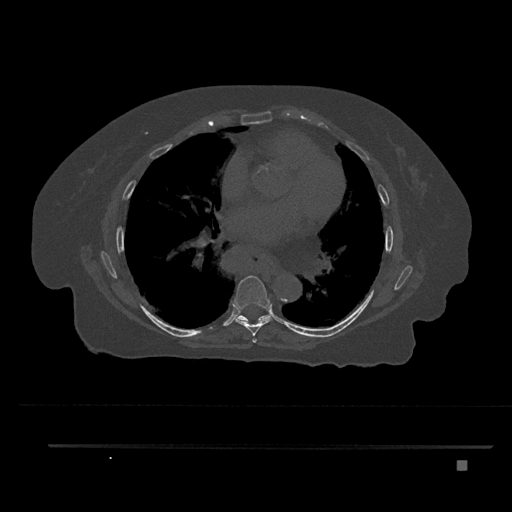
CT including the spine, one axial slice. Reconstruction kernel Br40s/3. 120 kVp. Bone window (W 1800 / L 400 HU). 0.5 mm slice thickness. 512 × 512 image matrix, field of view 437 × 437 mm. Female patient, age 76 years. From the clinical record (not read from this slice): primary cancer: lung; vertebrae with lytic lesions (as recorded): T11, L3.
Outlined on this slice (semi-automatic segmentation, software-assisted and operator-edited):
- T6 vertebra: box from (x=252, y=338) to (x=257, y=343) px
- T7 vertebra: (x=234, y=275)–(x=273, y=336)
- T8 vertebra: (x=237, y=314)–(x=270, y=321)